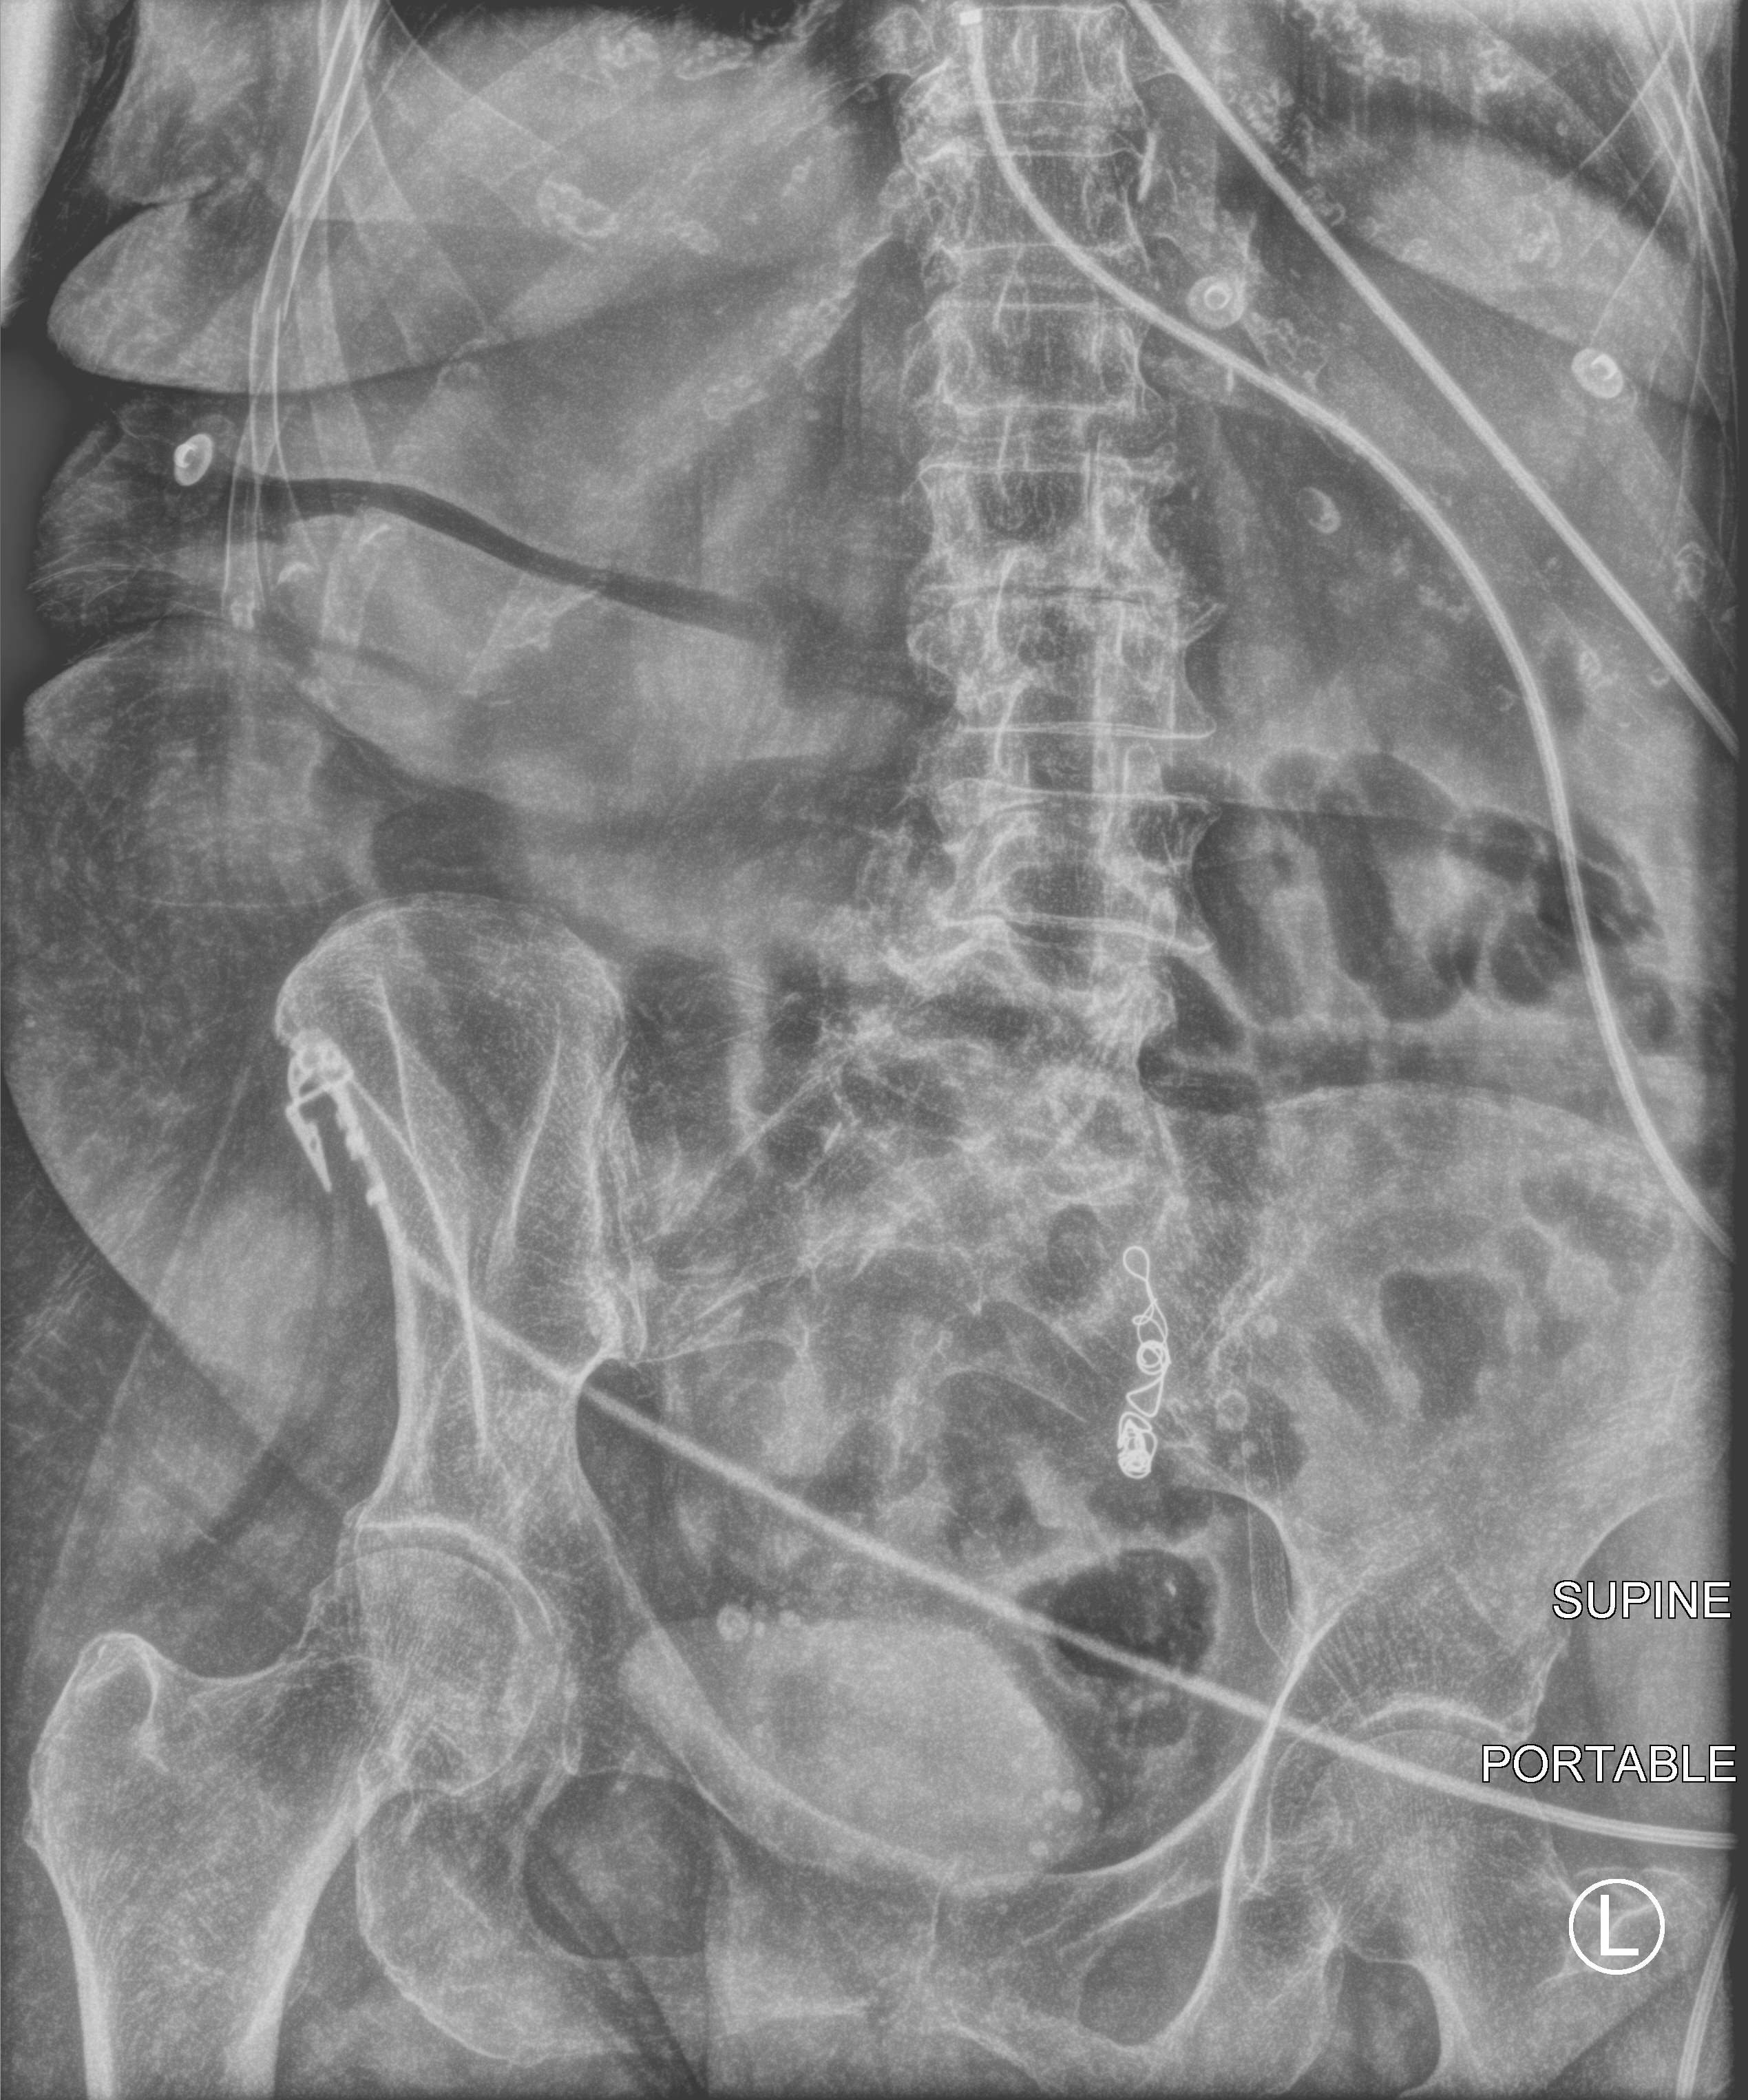
Bedside abdomen radiograph (computed radiography), anteroposterior (AP) projection. Female patient hospitalised with COVID-19, age 75–90 years.
From the hospital-stay record, not from the radiograph (when in the stay this image was taken is not recorded): mechanically ventilated during this hospital stay: no.